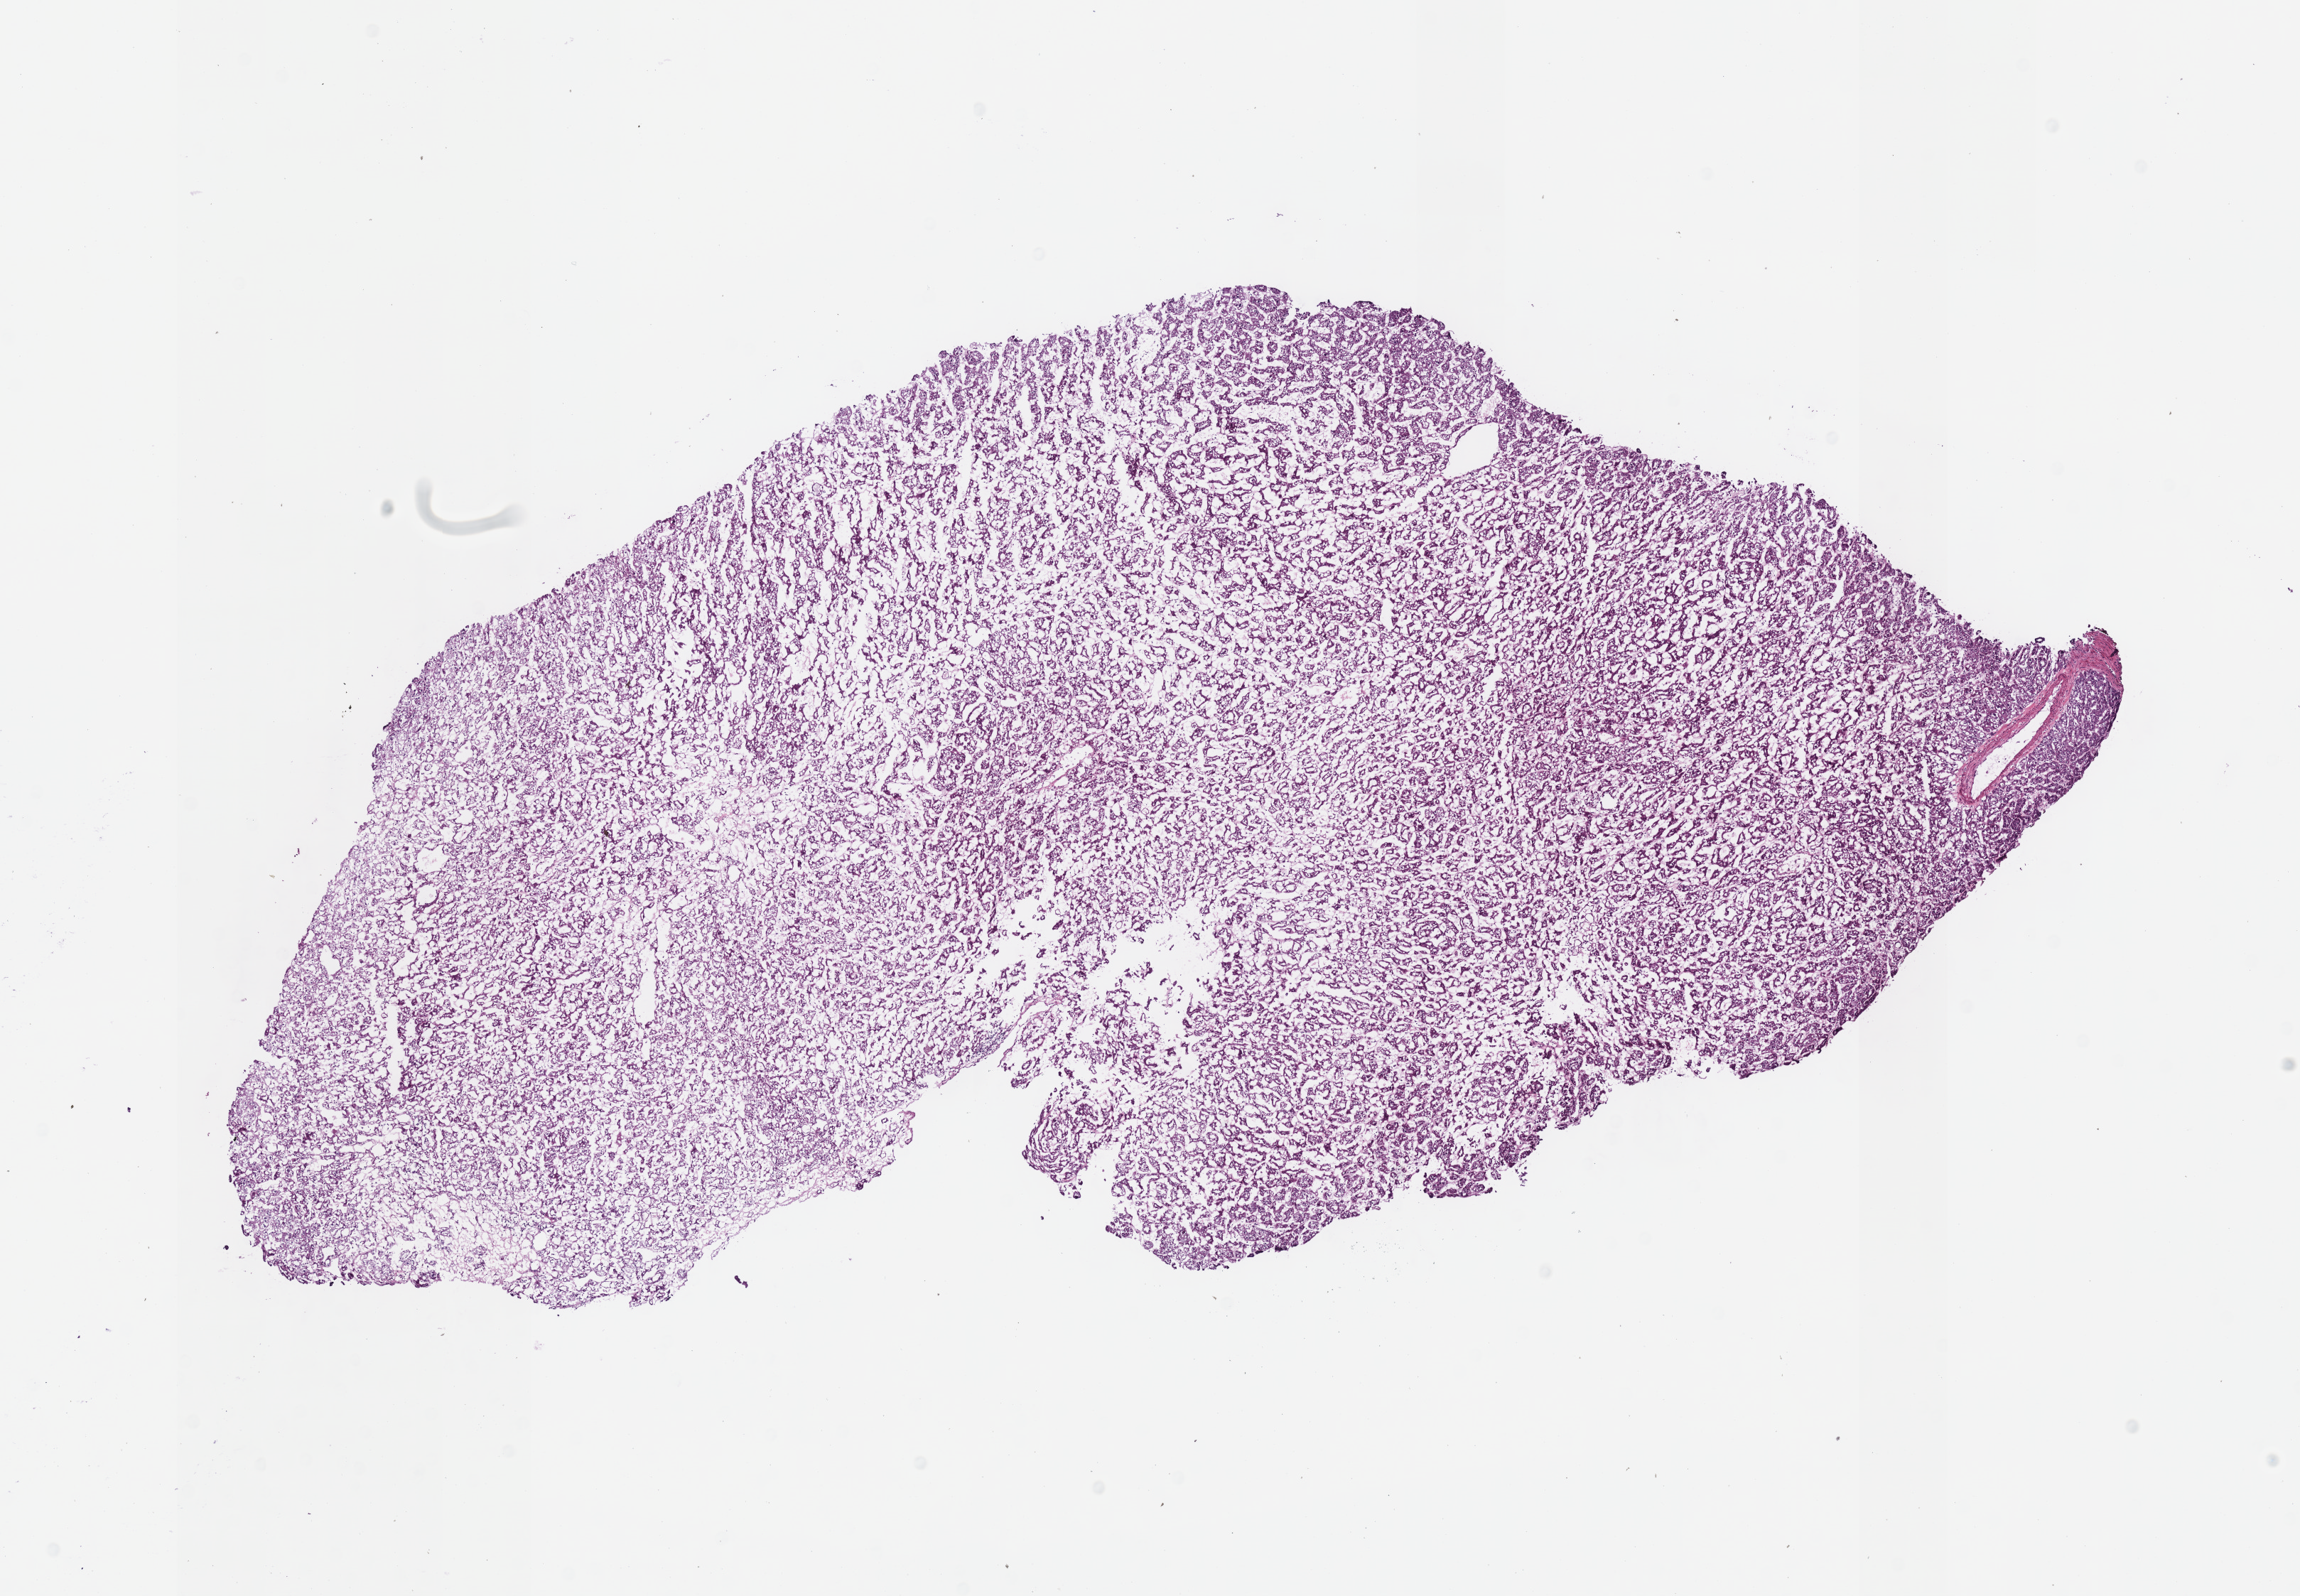
Whole-slide histology image, Hematoxylin and eosin (H&E) stained — shown as a low-resolution overview of the whole scanned area (about 12.7 x 8.8 mm), frozen section, sample: primary tumour, kidney. Male patient; age at initial diagnosis 67 years. Slide review estimates, as recorded: tumour cells 100%, tumour nuclei 90%, normal cells 0%, stromal cells 0%, necrosis 0%. Infiltration values recorded for this section: lymphocyte infiltration 1%, monocyte infiltration 0%, neutrophil infiltration 0%.
Pathologic diagnosis: Renal cell carcinoma, chromophobe type. TNM: T1a NX MX. AJCC pathologic stage: I (6th edition).